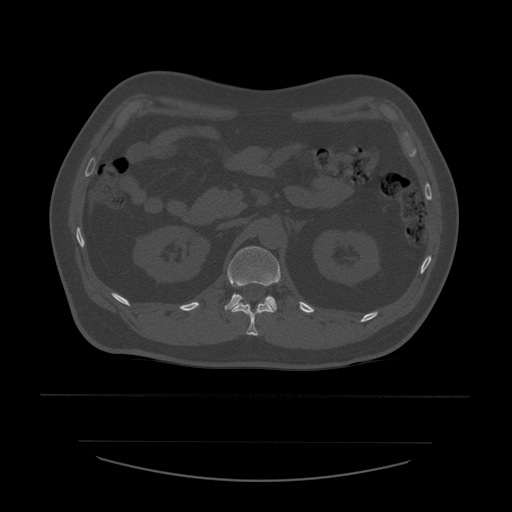
CT including the spine, one axial slice. Position 237 of 532 along the scan axis. Reconstruction kernel STANDARD. Bone window (W 1800 / L 400 HU). 1.25 mm slice thickness. 512 × 512 image matrix, field of view 441 × 441 mm. Patient age 44 years. Case-level facts recorded for this patient, not image findings: primary cancer: soft tissue sarcoma.
Outlined on this slice (semi-automatically segmented with operator editing):
- L1 vertebra: bounding box [x1, y1, x2, y2] px = [225, 247, 281, 313]
- T12 vertebra: [232, 300, 274, 336]